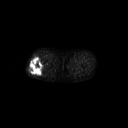
FDG PET of an extremity soft-tissue mass (from a PET/CT study), one axial slice; position 251 of 267 along the scan axis; 3.27 mm slice thickness; 128 × 128 image matrix, field of view 700 × 700 mm. Male patient, age 43 years. From the clinical record (not read from this slice): histological type: poorly differentiated synovial sarcoma; grade: high; site of the primary tumour: right buttock.
Structures marked on this image (expert contour drawn on MRI and transferred to this co-registered scan by the dataset authors):
- gross tumour volume including surrounding oedema: bounding box (x1, y1, x2, y2) in pixels: (29, 57, 45, 75)
- gross tumour volume (mass): (29, 57, 44, 75)